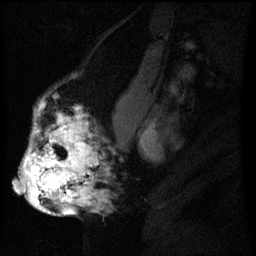
Breast MRI (dynamic contrast-enhanced), one sagittal slice. Dynamic contrast-enhanced series, image 2 of 3 at this slice position (ordered by acquisition). 1.5 T. TE 4.2 ms, TR 8 ms. 2.2 mm slice thickness. 256 × 256 image matrix. Female patient, age 50 years.
Outlined on this slice (semi-automatically segmented with operator editing):
- analysis volume of interest (the breast-tissue region the enhancement analysis was run in; not a lesion): bounding box (x1, y1, x2, y2) in pixels: (23, 112, 95, 211)
- tumour enhancement mask (voxels above the 70 % enhancement threshold inside the analysis volume of interest): (23, 118, 92, 211)